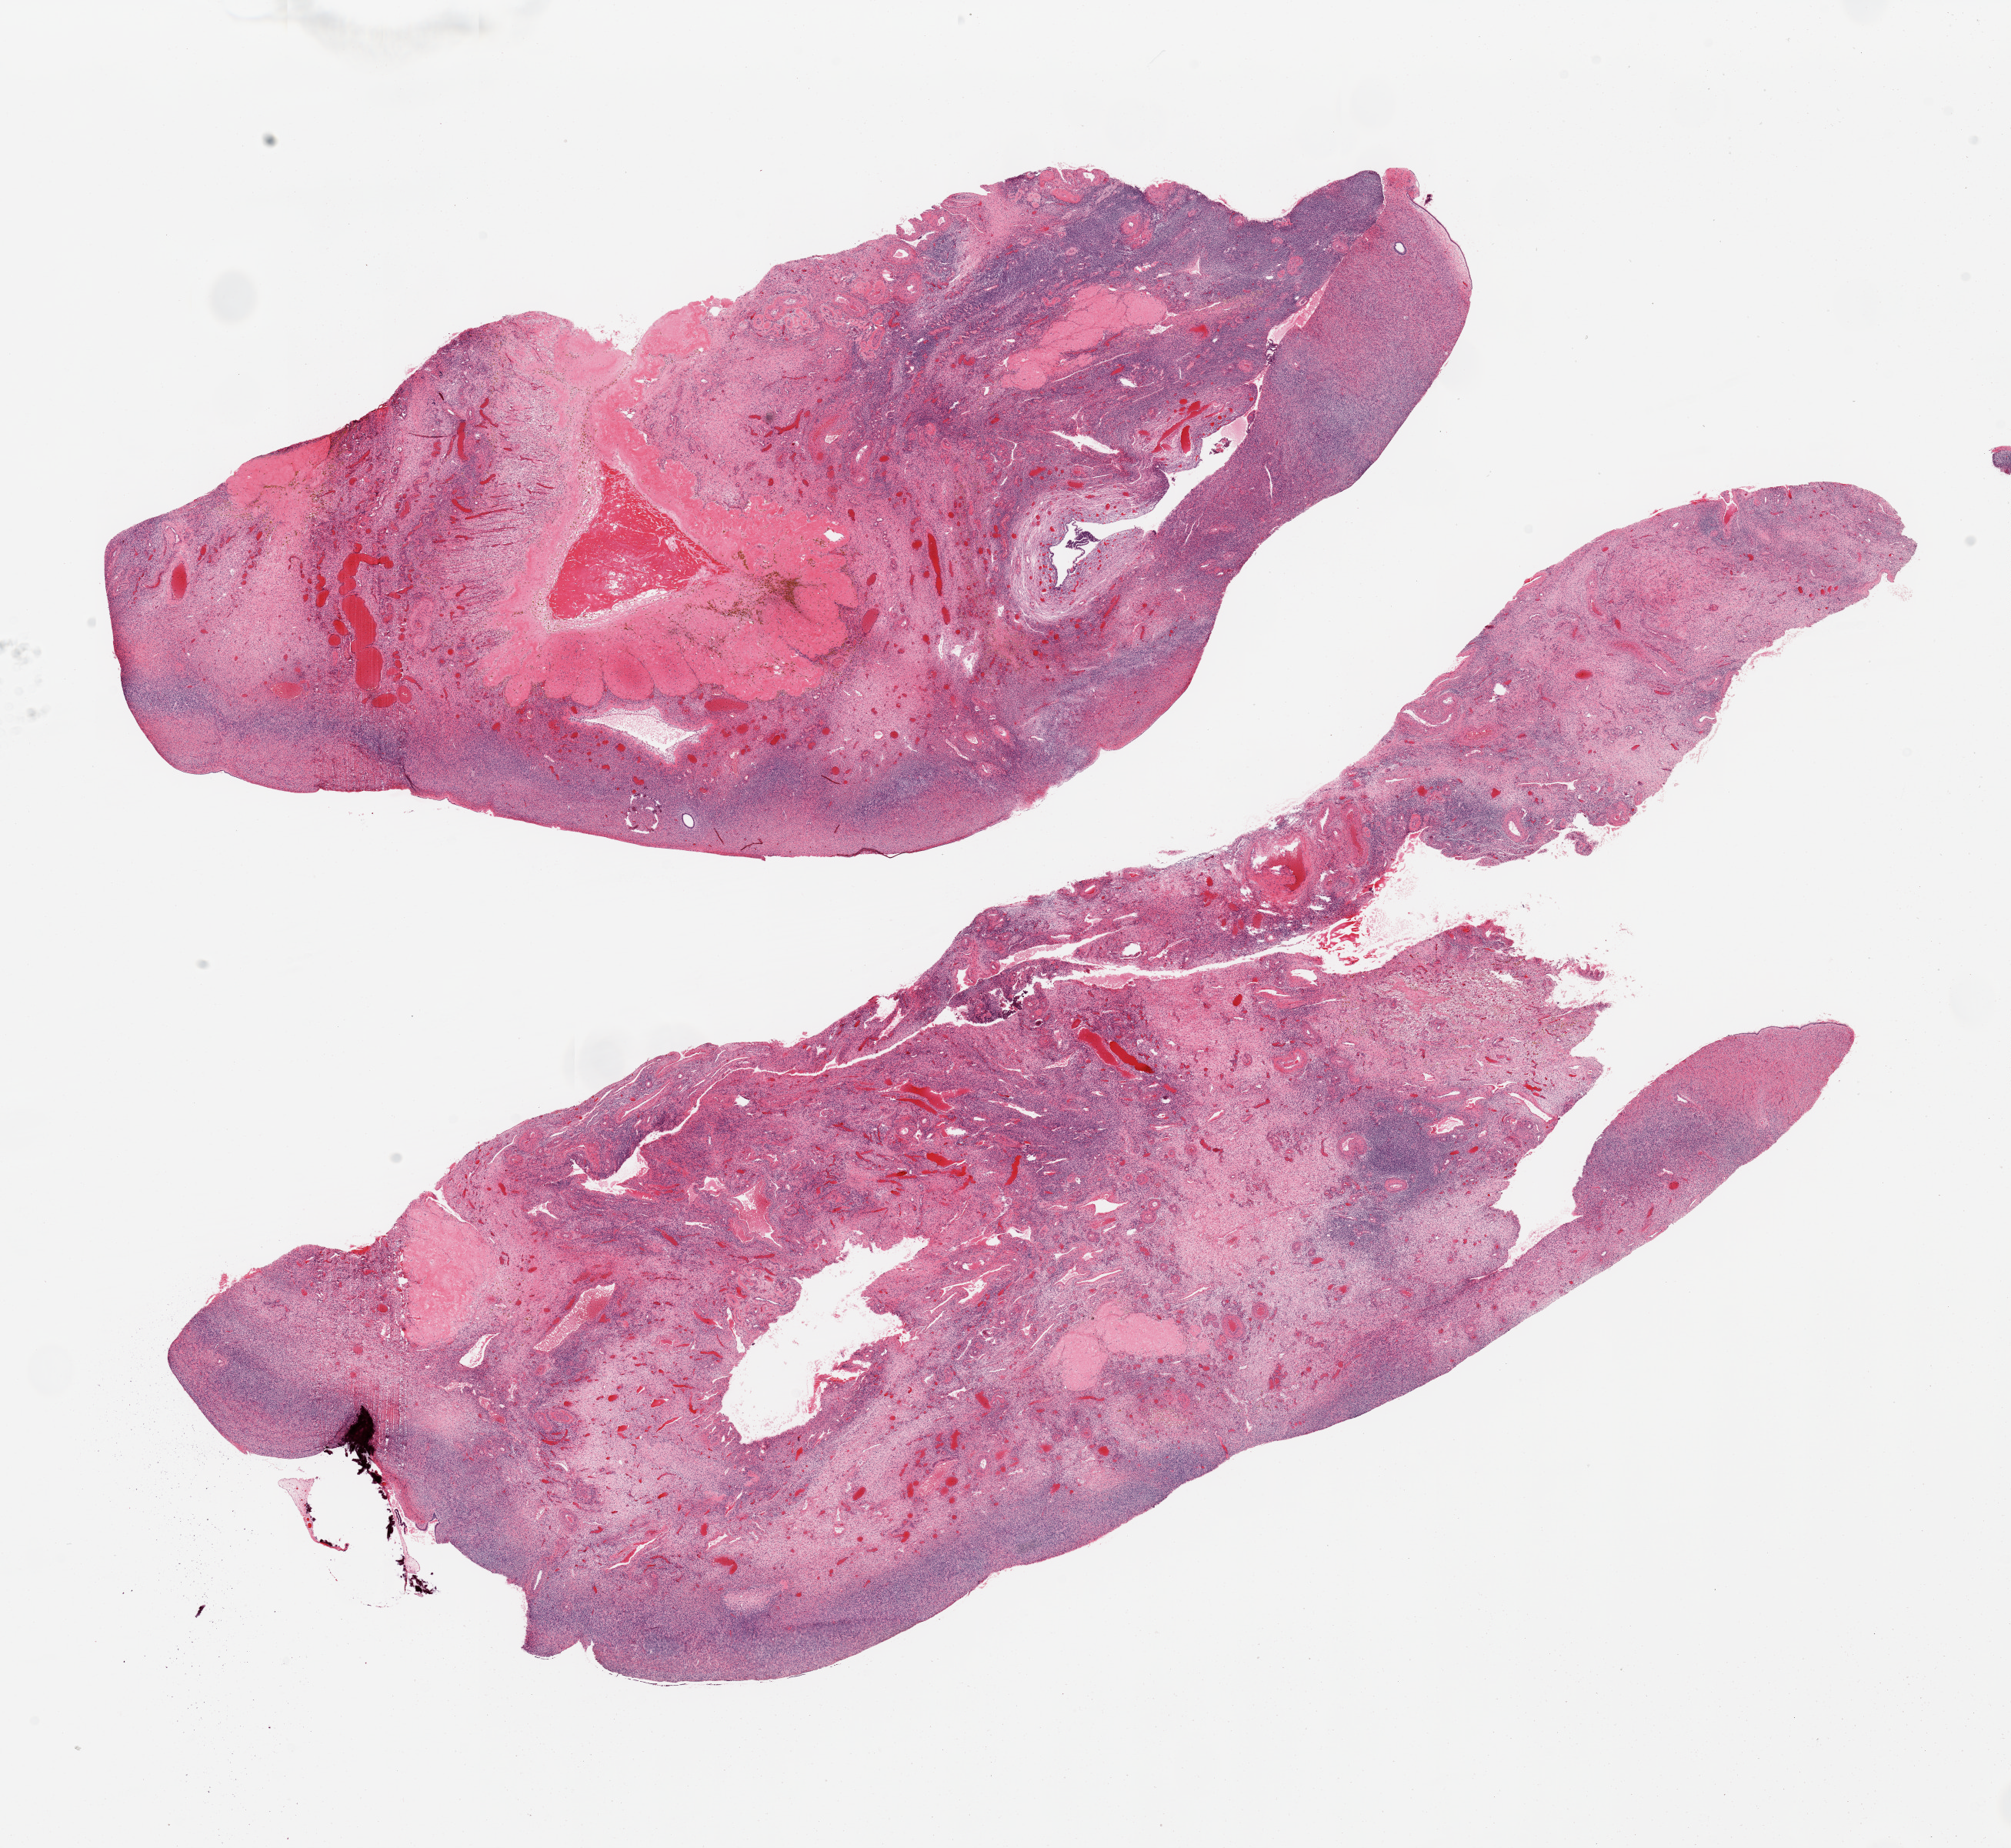
Digitized haematoxylin and eosin-stained section, shown as a low-resolution overview of the whole scanned area (about 20.7 x 19.0 mm); PAXgene-fixed, paraffin-embedded tissue; target tissue: ovary; tissue donor sample.
Pathologist's review note for this sample: 2 pieces, late stage resolving hemorrhagic corpus luteum.